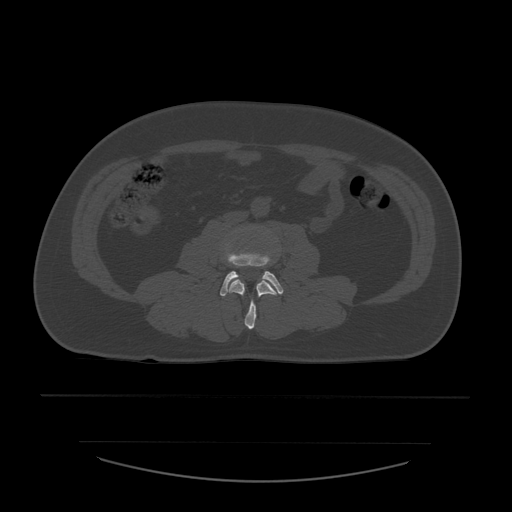
CT including the spine, one axial slice; position 160 of 532 along the scan axis; reconstruction kernel STANDARD; 120 kVp; bone window (W 1800 / L 400 HU); 512 × 512 image matrix, field of view 441 × 441 mm. Patient age 44 years. From the clinical record (not read from this slice): primary cancer: soft tissue sarcoma.
Outlined on this slice (semi-automatically segmented with operator editing):
- L3 vertebra: bounding box (x1, y1, x2, y2) in pixels: (228, 279, 277, 330)
- L4 vertebra: (220, 244, 284, 297)